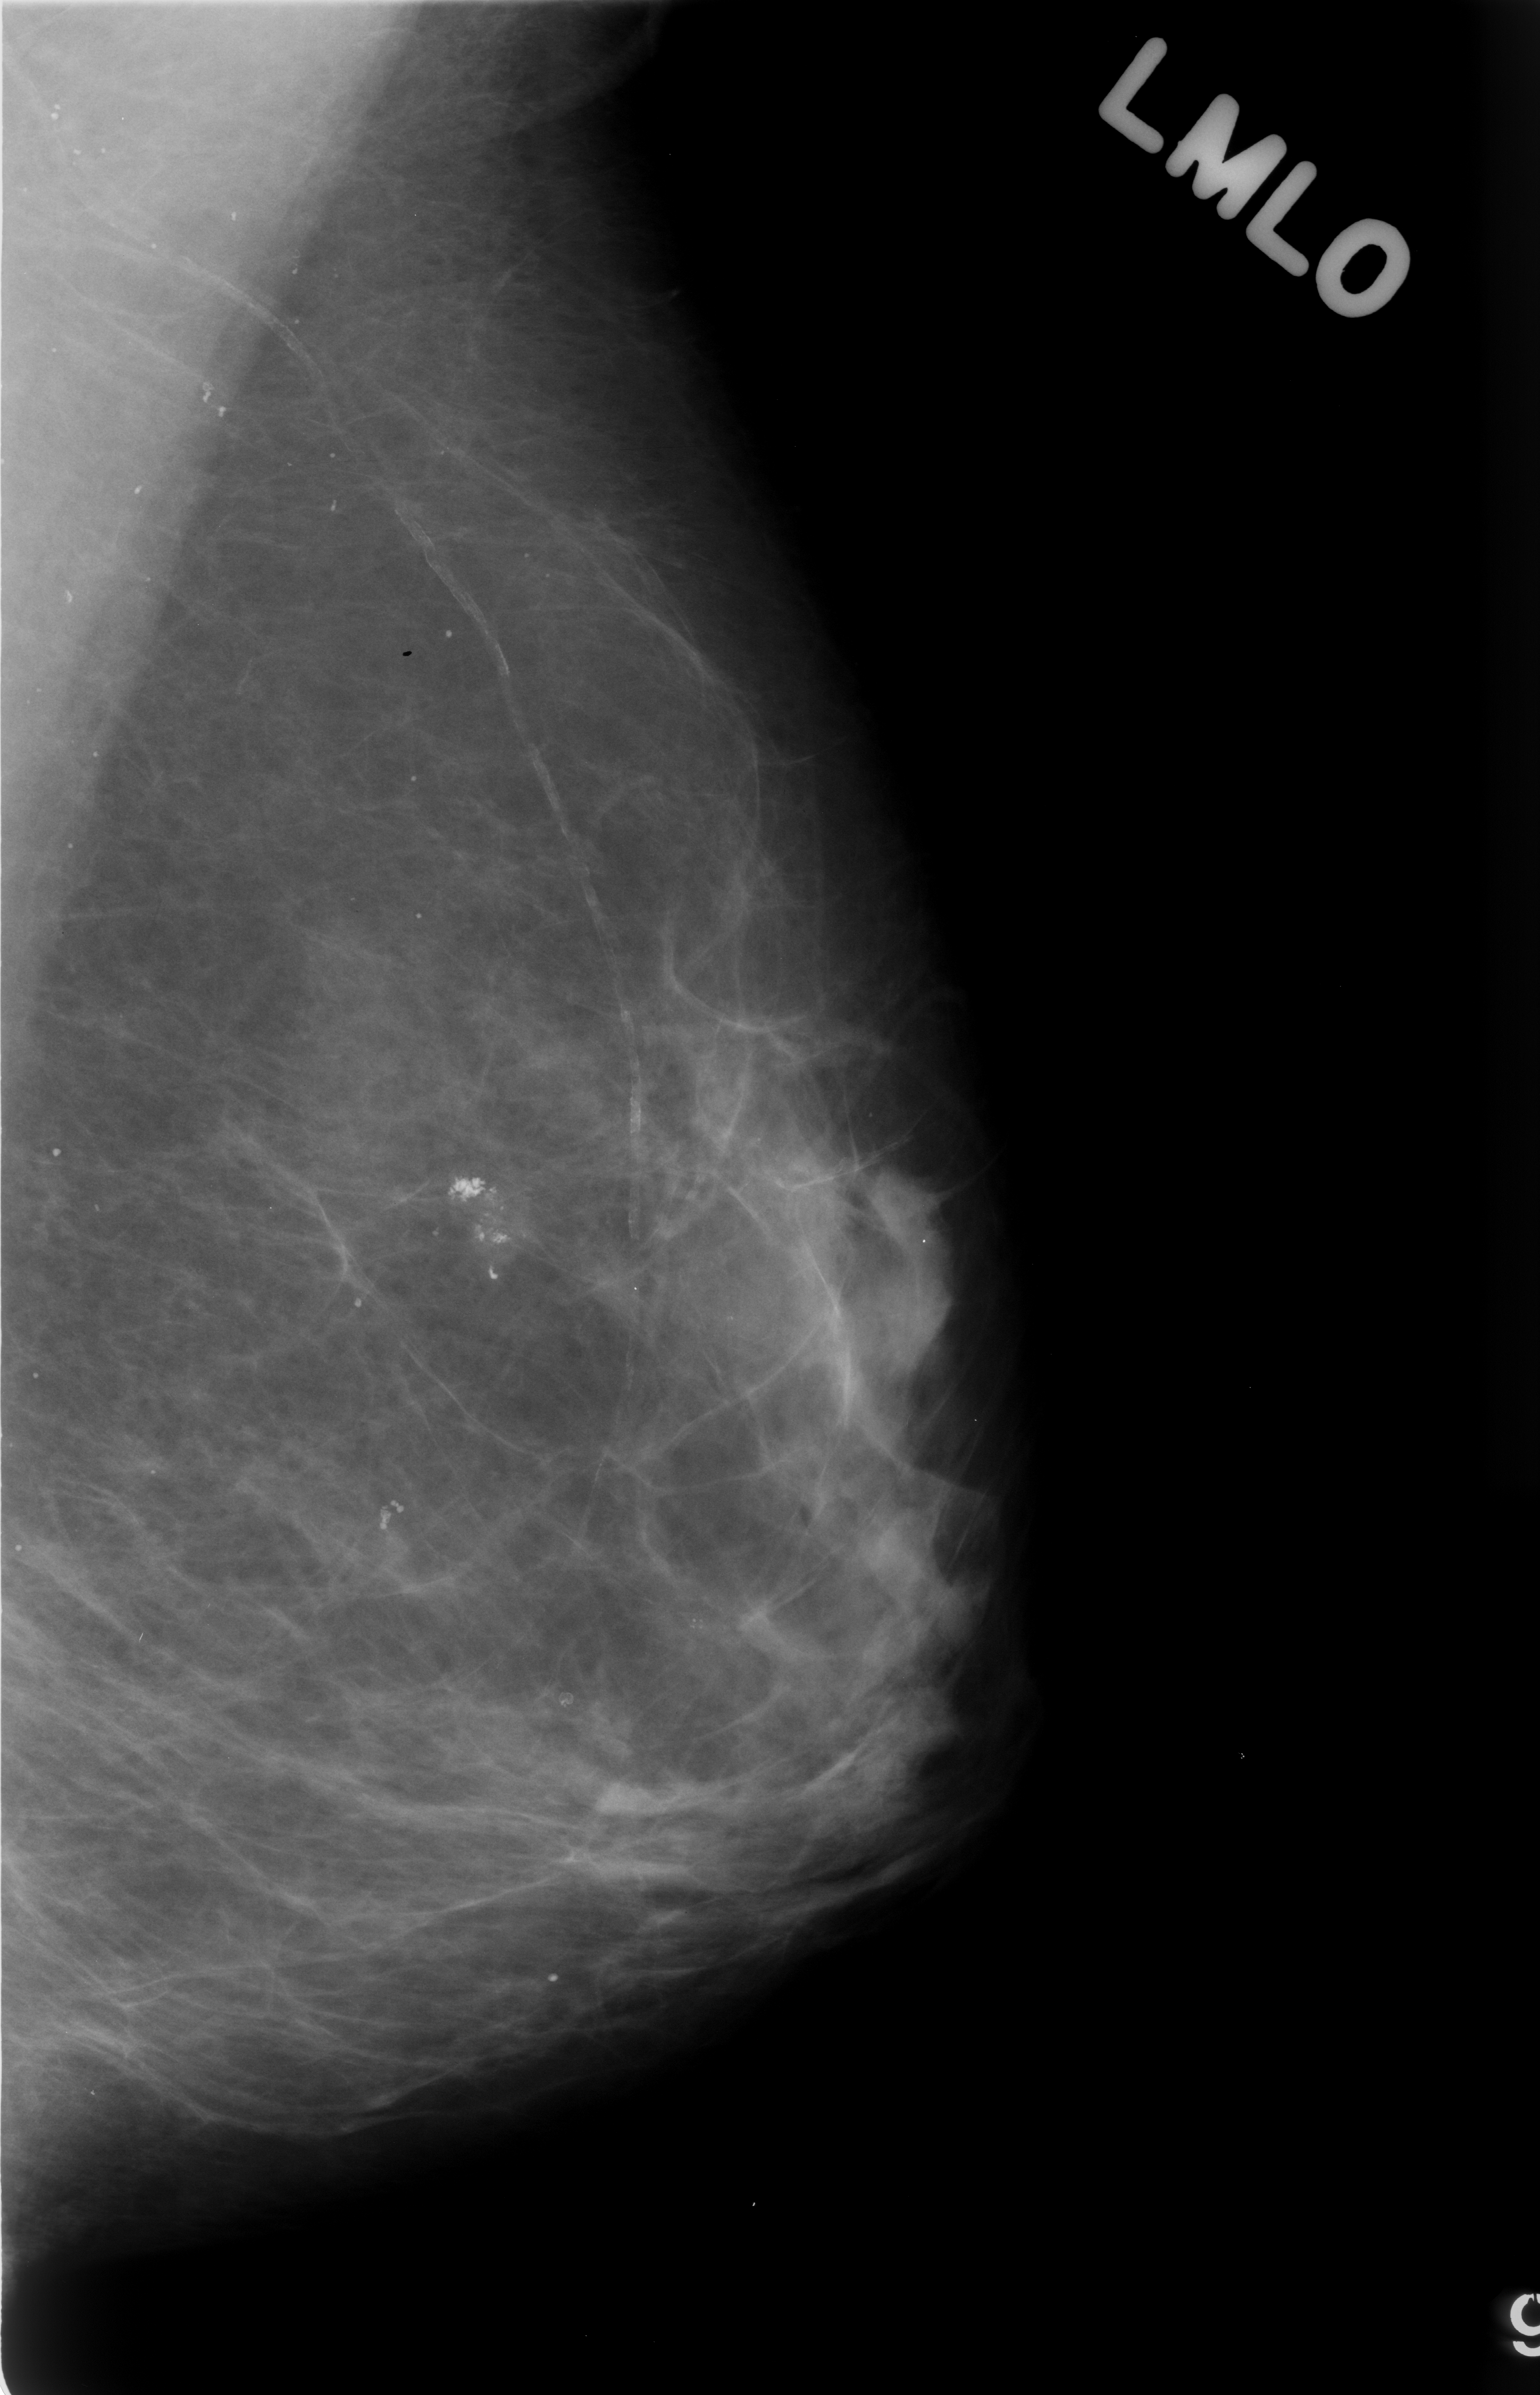
Scanned film-screen mammogram. Left breast. MLO view. Breast composition: almost entirely fatty (BI-RADS density category 1 of 4). 1540 × 2395 image matrix.
Expert-marked regions of interest on this image (one box per marked abnormality):
- calcifications, morphology pleomorphic, distribution clustered; BI-RADS assessment category 3; pathology result (as recorded, not read from the image): benign: box from (x=353, y=1071) to (x=597, y=1354) px